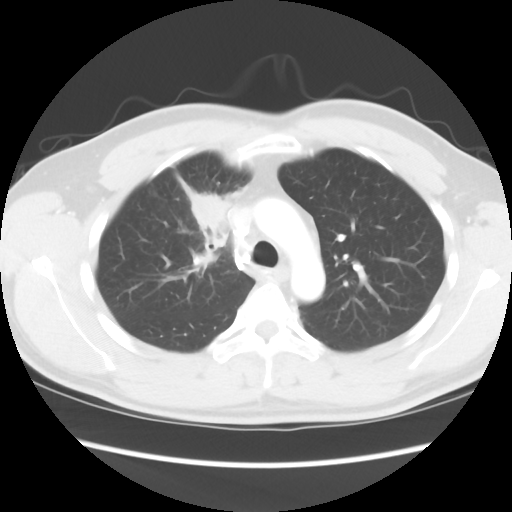
Chest CT, one axial slice. Slice 64 of 80 in the series (ordered by position). Reconstruction kernel STANDARD. 120 kVp. Lung window (W 1500 / L -600 HU). 5 mm slice thickness. 512 × 512 image matrix. Patient: male, 35 years. Case-level facts recorded for this patient, not image findings: clinical TNM (as recorded): T1c N1 M1b.
Annotated regions visible in this slice (rectangle marked by the reading radiologist):
- lung tumour (recorded histology: adenocarcinoma): bounding box [x1, y1, x2, y2] px = [182, 184, 231, 241]